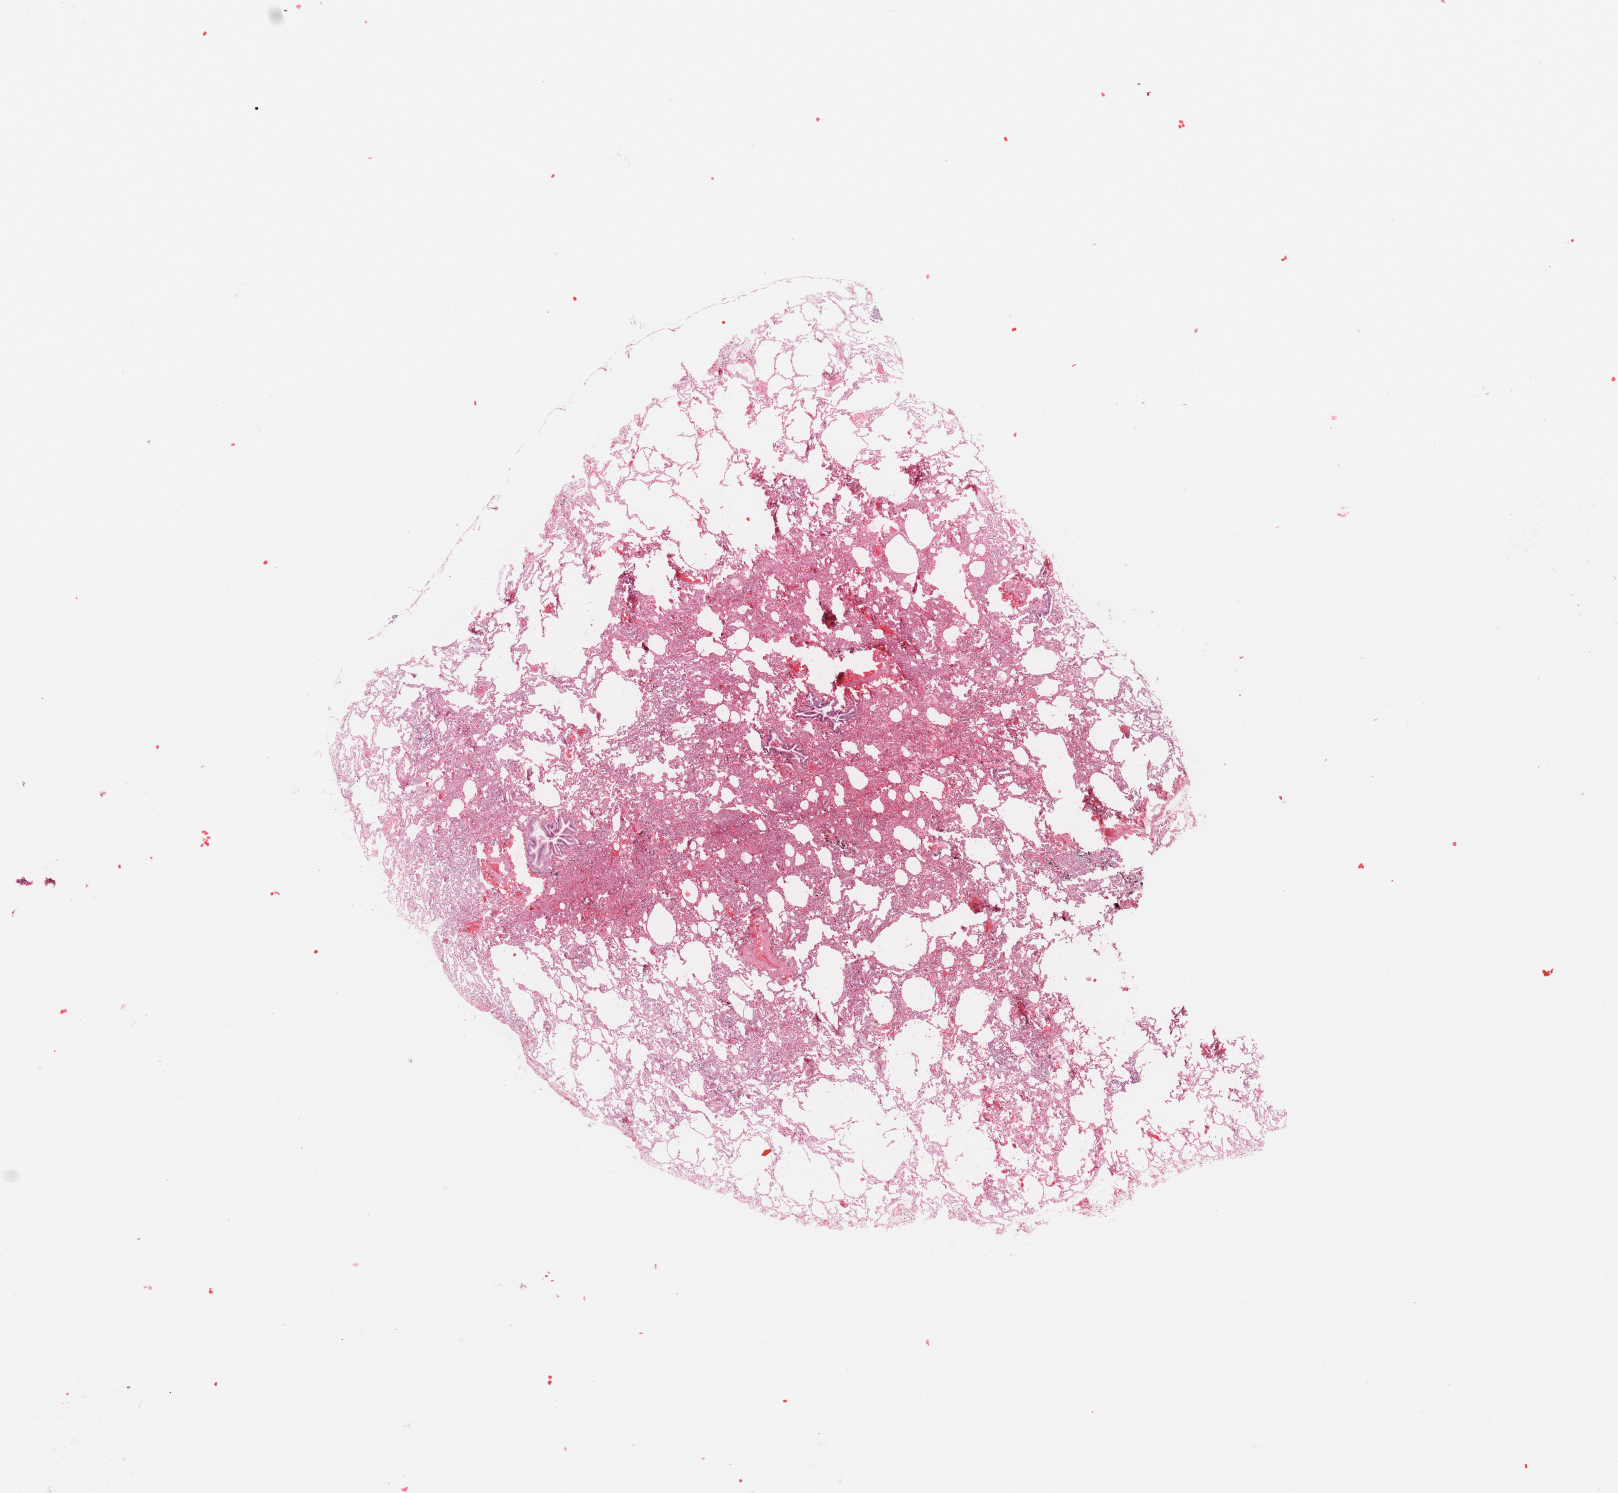
Whole-slide histology image, H&E-stained, shown as a low-resolution overview of the whole scanned area (about 12.8 x 11.8 mm). Normal (non-tumour) tissue sample, sampled site: lung. Patient: male, age 44 years.
This section: normal (non-tumour) tissue from the same patient. Patient diagnosis: Squamous cell carcinoma, NOS.